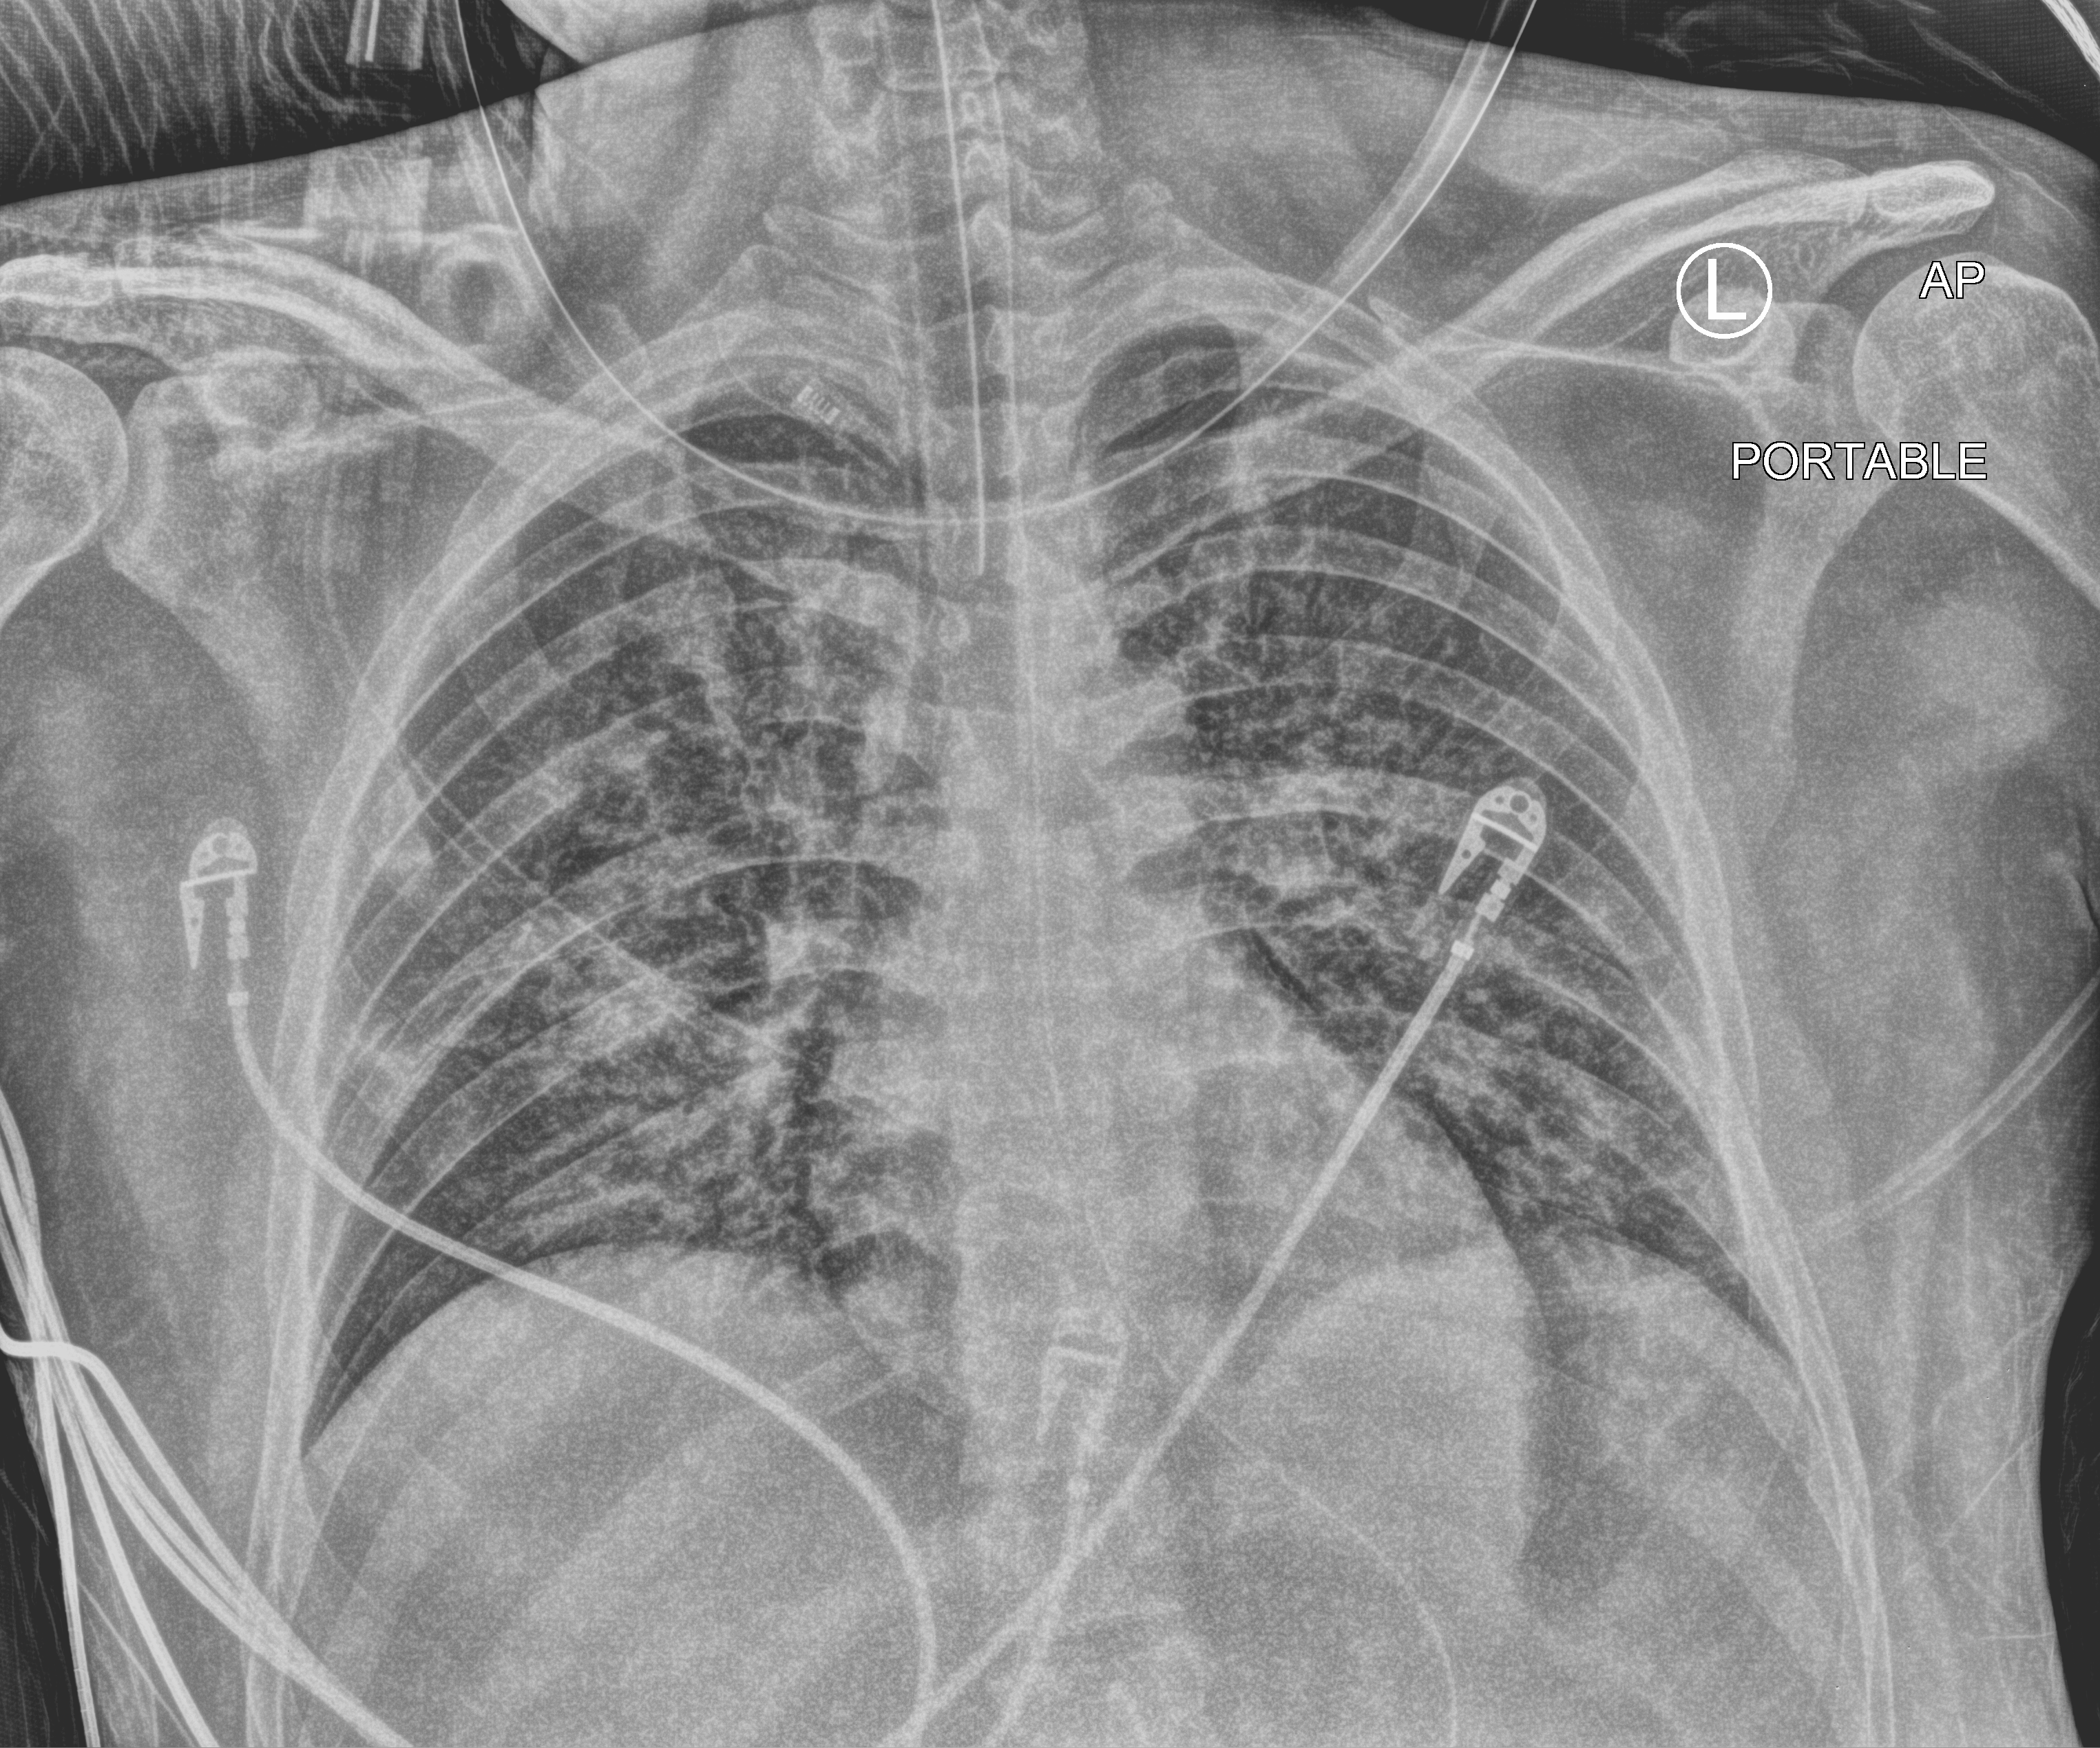
Chest X-ray (portable), anteroposterior (AP) projection. Adult patient hospitalised with COVID-19, age 18–59 years.
Admission-level facts for this patient (not findings on this image; timing relative to this image not recorded):
- smoking status (admission record): never
- mechanically ventilated during this hospital stay: yes
- admitted to intensive care during this hospital stay: yes